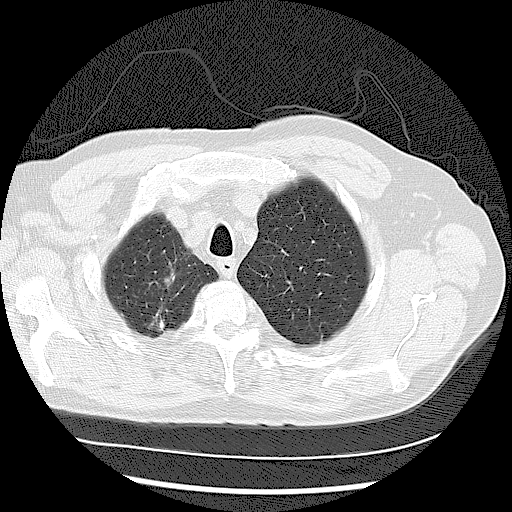
Low-dose screening chest CT, one axial slice. Slice 100 of 122 in the series (ordered by position). 120 kVp. Lung window (W 1500 / L -600 HU). 2.5 mm slice thickness. 512 × 512 image matrix, field of view 360 × 360 mm.
Structures marked on this image (outlined manually by an expert reader):
- lesion 2 (tumor, upper lobe of right lung): bounding box (x1, y1, x2, y2) in pixels: (164, 259, 175, 287)